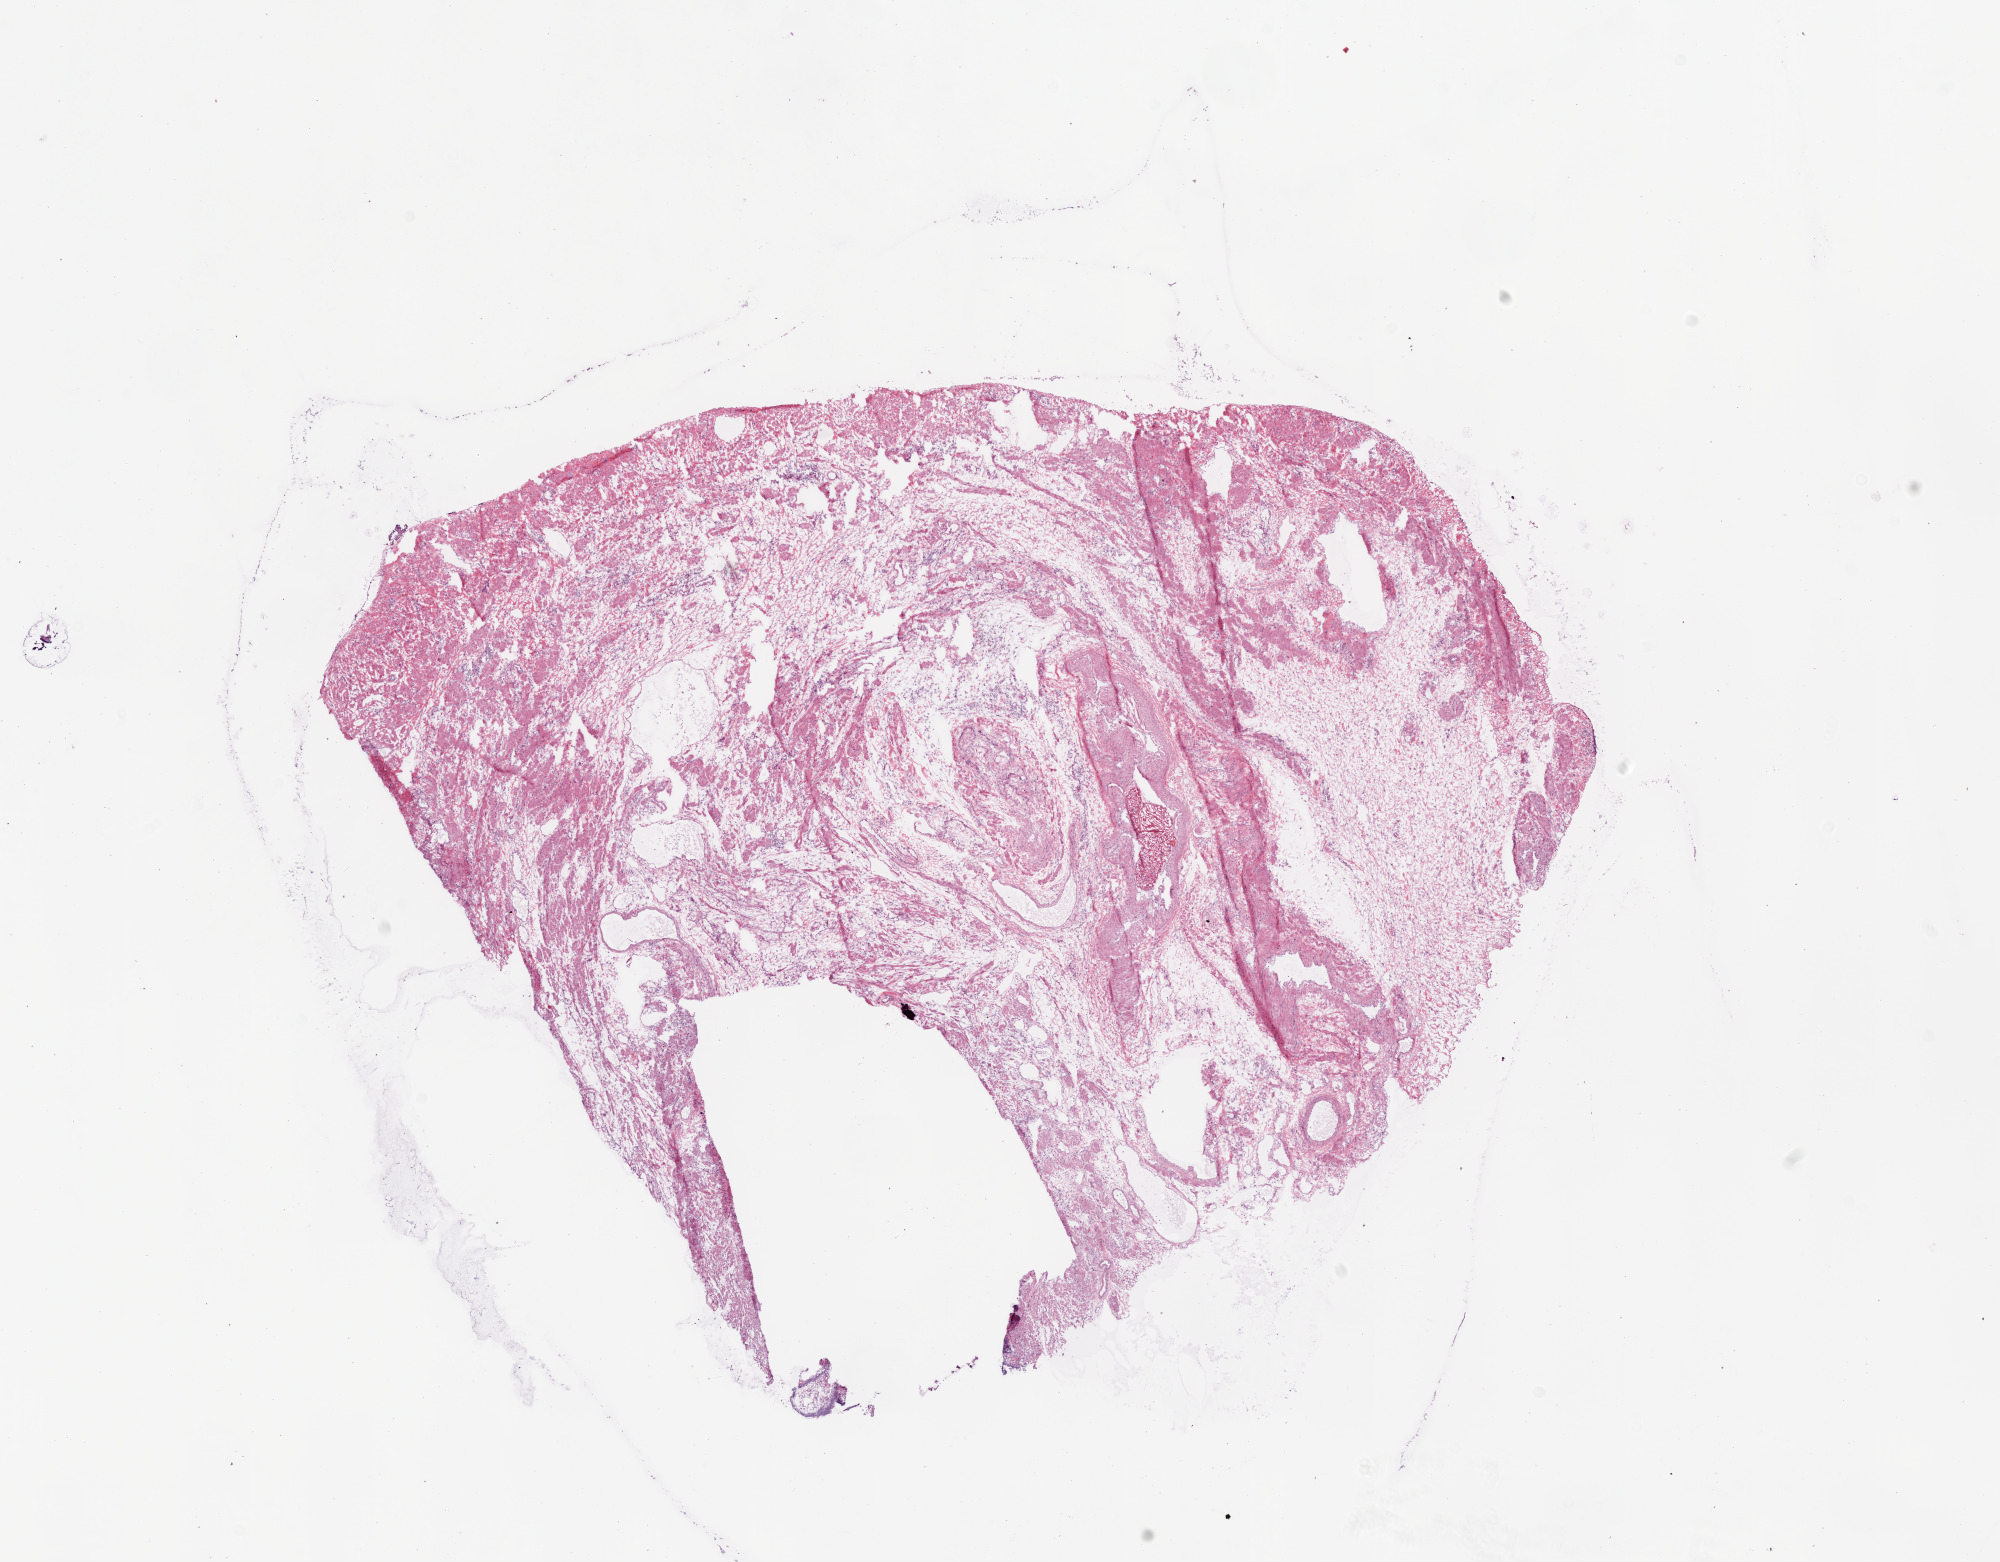
Digitized H&E tissue section (whole slide) — whole scanned area (about 16.0 x 12.5 mm, acquisition: 20x scan) shown as a low-resolution overview. Frozen section from the bottom of the tissue portion. Sample: solid tissue normal (non-tumour tissue), ovary. Patient: female, age at initial diagnosis 81 years.
• this section: solid tissue normal sample (biorepository sample class)
• patient diagnosis: Serous cystadenocarcinoma, NOS